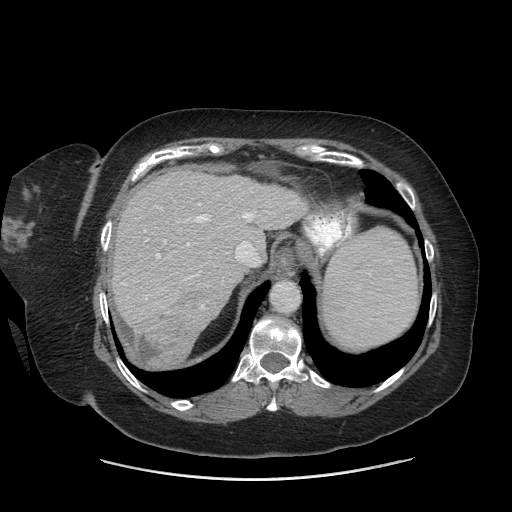
Contrast-enhanced abdominal CT (liver protocol), one axial slice; slice 56 of 69 in the series (ordered by position); reconstruction kernel STANDARD; 140 kVp; soft-tissue window (W 400 / L 40 HU); 512 × 512 image matrix, field of view 420 × 420 mm. Case-level facts recorded for this patient, not image findings: diagnosis: hepatocellular carcinoma (patient treated with transarterial chemoembolisation; whether this scan precedes or follows treatment is not stated here); TNM stage (as recorded): Stage-IIIB; Child-Pugh class: A; tumour differentiation: moderately differentiated.
Annotated regions visible in this slice (semi-automatically segmented with operator editing):
- liver parenchyma outside the tumour (the mass and vessels are separate outlines, so this box may not span the whole liver): bounding box <112,168,306,366> (left, top, right, bottom; pixels)
- mass: <135,309,194,365>
- liver vessels: <123,203,260,308>